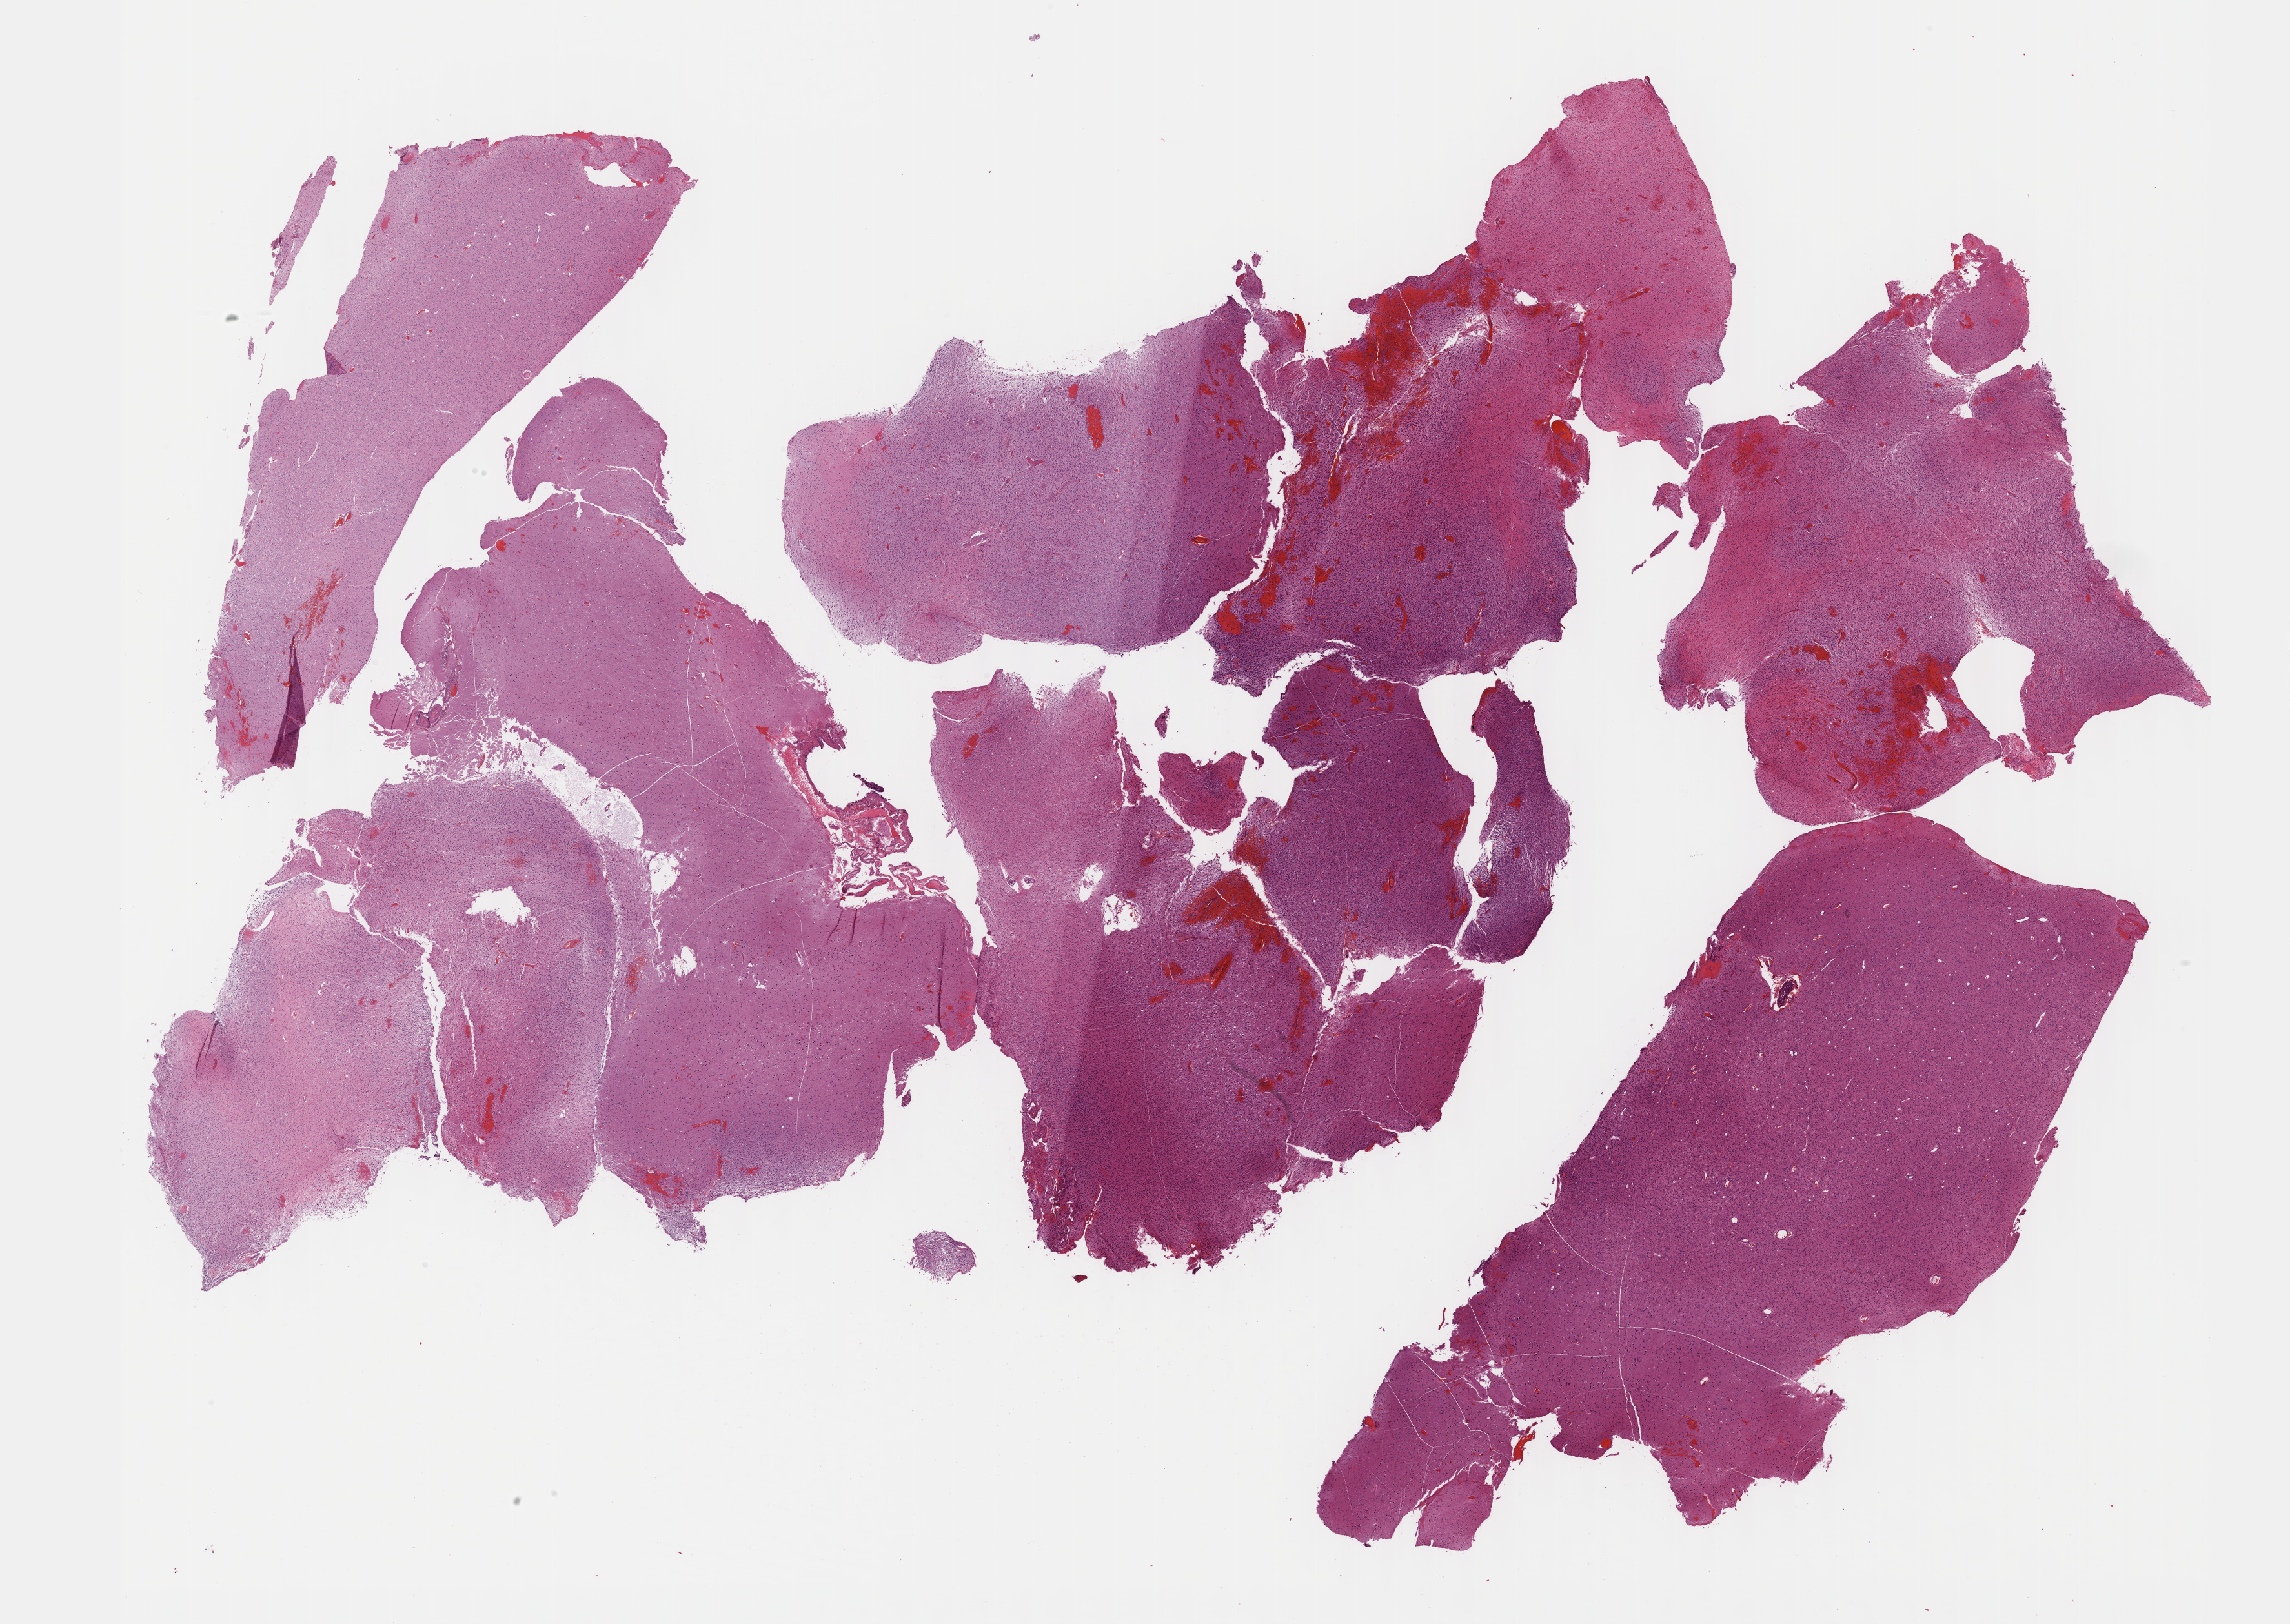
Whole-slide histology image, Hematoxylin and eosin (H&E) stained — a low-resolution overview of the entire scanned area, about 28.7 x 20.3 mm, formalin-fixed paraffin-embedded (FFPE) diagnostic section, brain, primary tumour sample. Patient: male, age at initial diagnosis 43 years. Histologic grade: G2 (moderately differentiated).
Pathologic diagnosis: Mixed glioma (cerebrum).